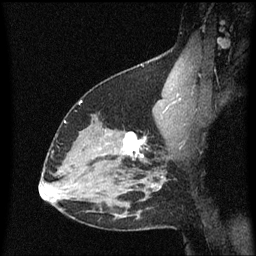
Breast MRI (dynamic contrast-enhanced), one sagittal slice. Slice 42 of 60 in the series (ordered by position). Dynamic contrast-enhanced series, image 2 of 3 at this slice position (ordered by acquisition). 1.5 T. TE 4.2 ms, TR 8.4 ms. 2 mm slice thickness. 256 × 256 image matrix, field of view 200 × 200 mm. Patient: female, 38 years. From the clinical record (not read from this slice): setting: breast cancer imaged before/during neoadjuvant chemotherapy; receptor status: HR-positive, HER2-negative.
Annotated regions visible in this slice (semi-automatically segmented with operator editing):
- analysis volume of interest (the breast-tissue region the enhancement analysis was run in; not a lesion): box from (x=122, y=130) to (x=150, y=163) px
- tumour enhancement mask (voxels above the 70 % enhancement threshold inside the analysis volume of interest): (x=124, y=132)–(x=149, y=159)